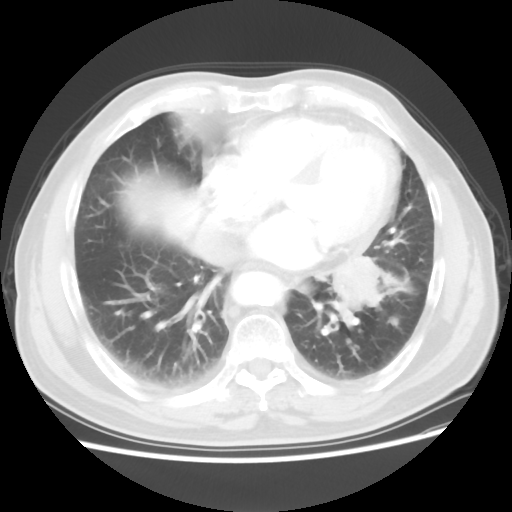
Chest CT, one axial slice. 120 kVp. Lung window (W 1500 / L -600 HU). 5 mm slice thickness. 512 × 512 image matrix, field of view 360 × 360 mm. Male patient, age 75 years. From the clinical record (not read from this slice): clinical TNM (as recorded): T3 N0 M0.
Structures marked on this image (bounding box drawn by a radiologist):
- lung tumour (recorded histology: squamous cell carcinoma): box from (x=319, y=250) to (x=395, y=310) px